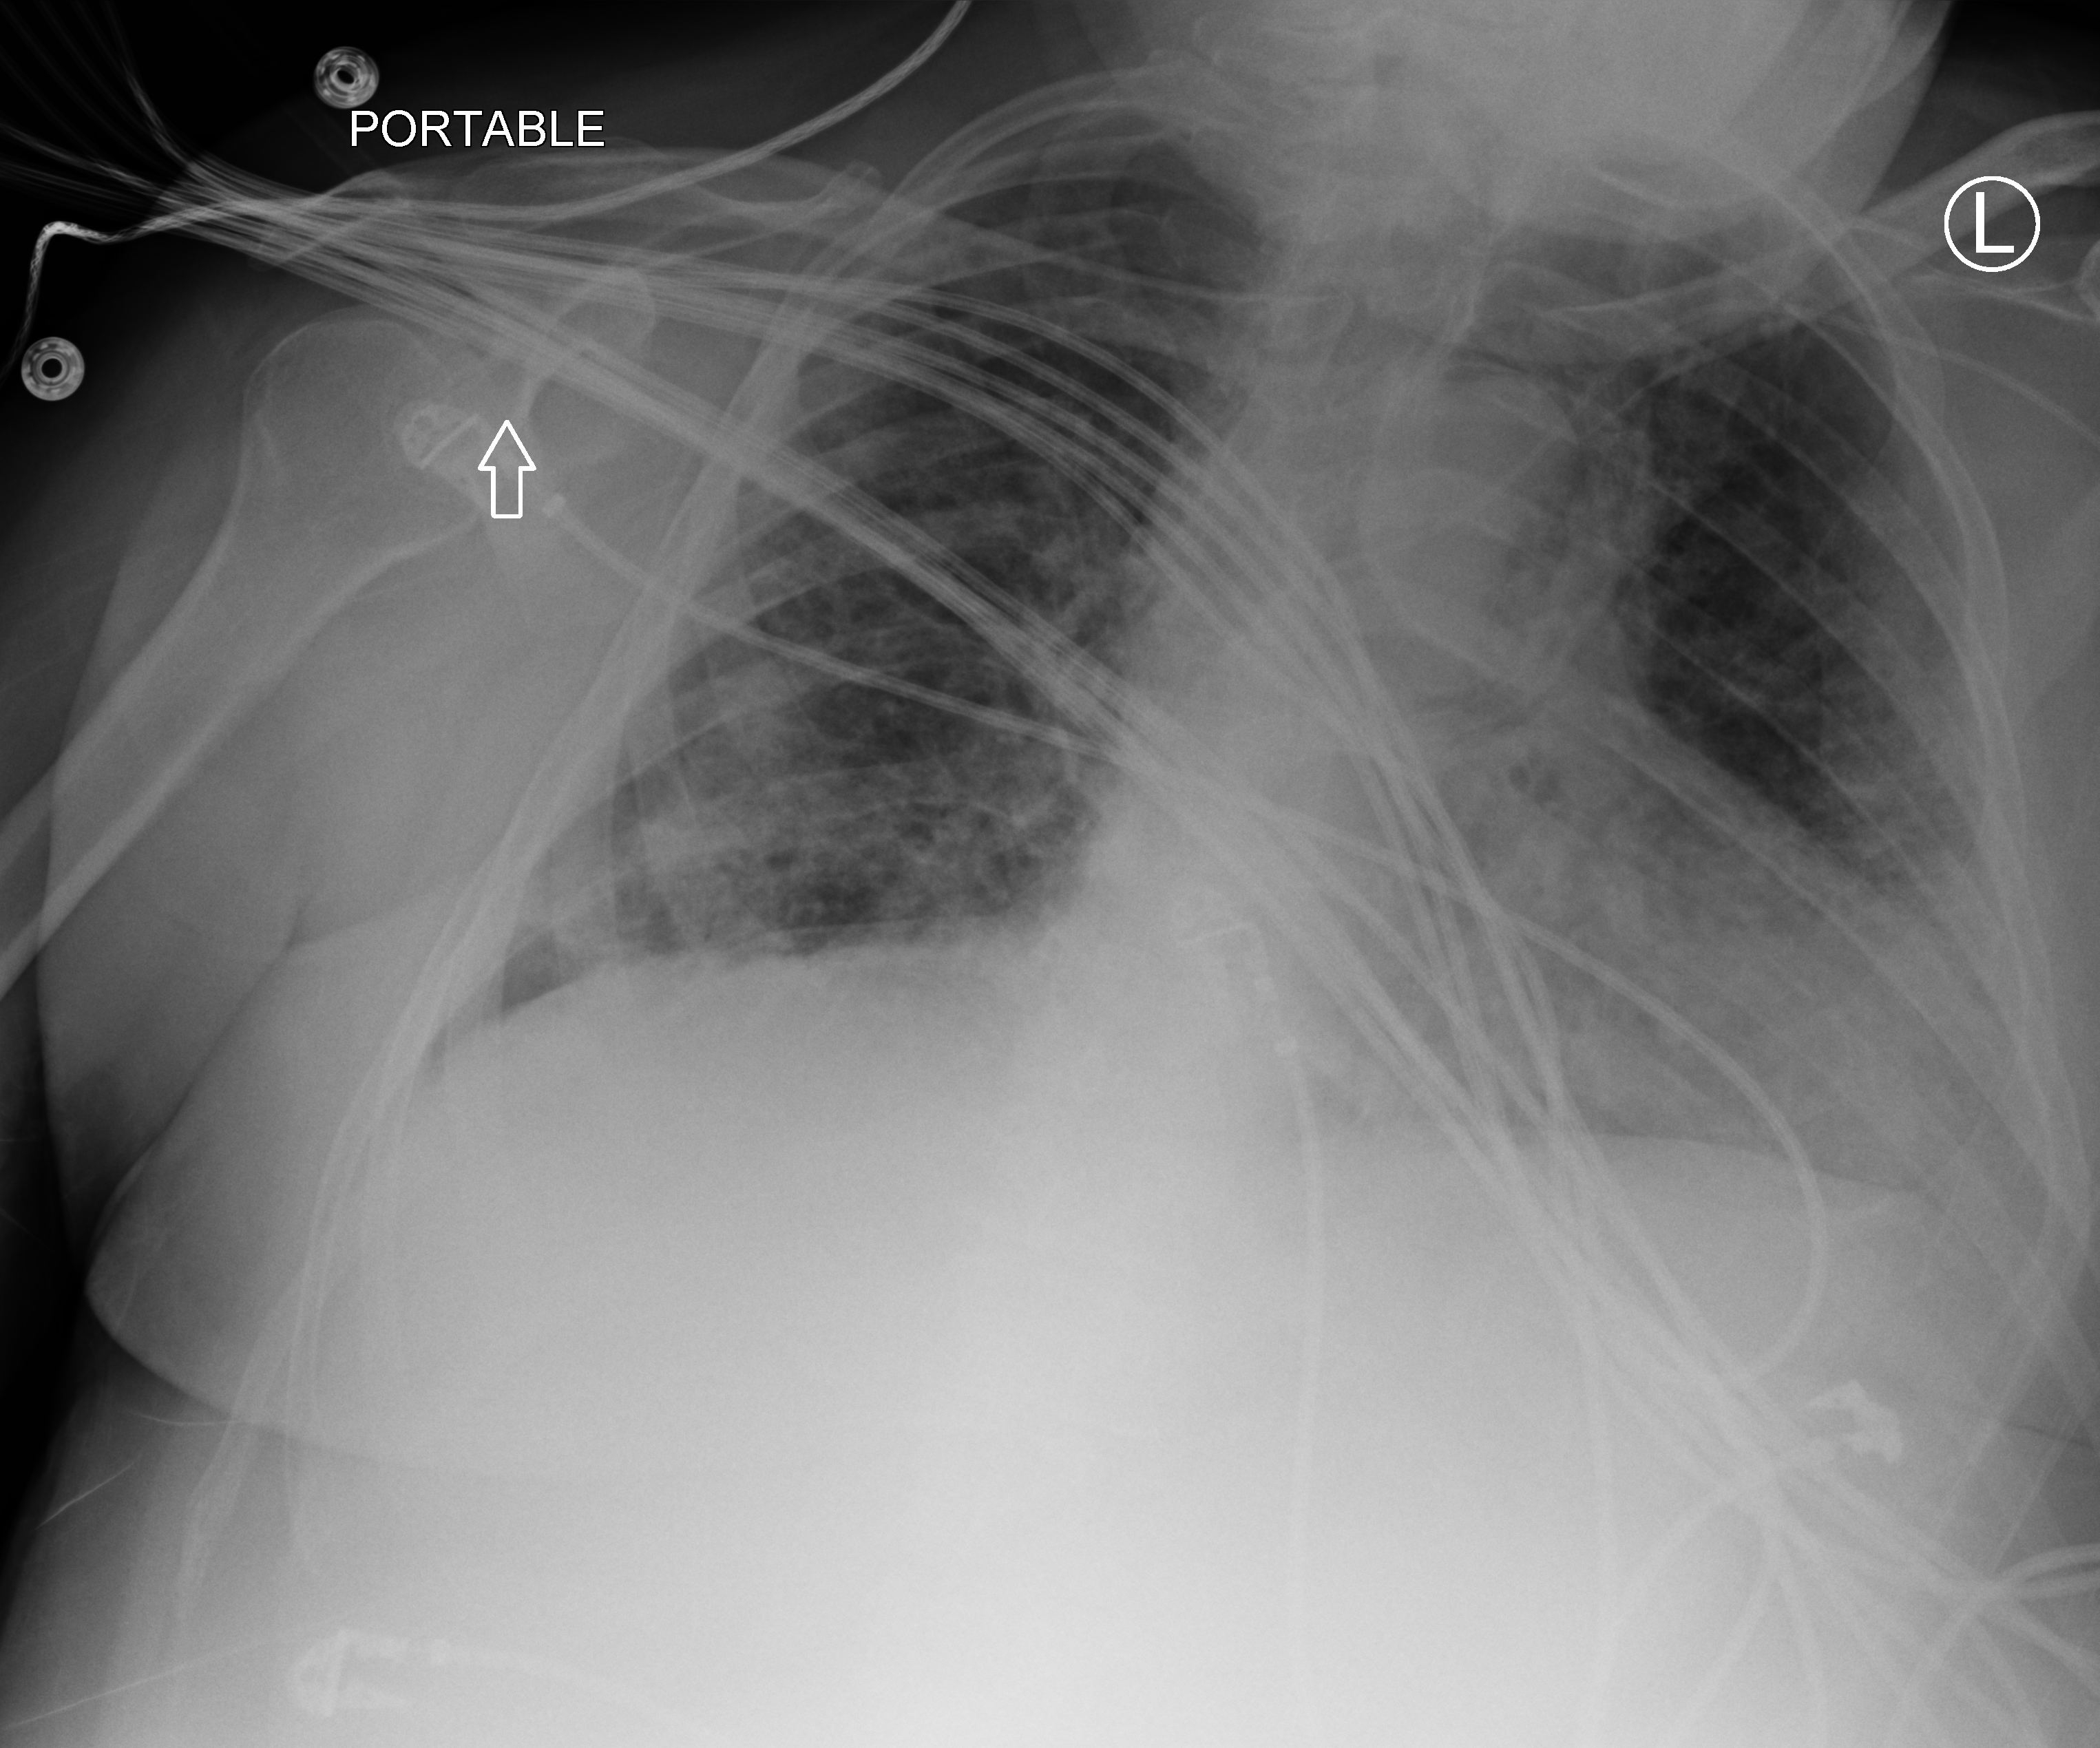
Portable chest radiograph, anteroposterior (AP) projection. Patient hospitalised with COVID-19; male, aged 18–59 years.
Hospital-stay facts (about this admission, not read from this image; timing relative to this image not recorded): chronic kidney disease (admission record): no; smoking status (admission record): never.